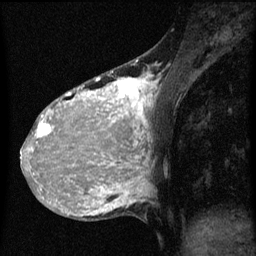
Breast MRI (dynamic contrast-enhanced), one sagittal slice. Slice 20 of 60 in the series (ordered by position). Dynamic contrast-enhanced series, image 2 of 3 at this slice position (ordered by acquisition). 1.5 T. TE 4.2 ms, TR 8 ms. 256 × 256 image matrix, field of view 180 × 180 mm. Patient: female, 36 years.
Outlined on this slice (semi-automatically segmented with operator editing):
- analysis volume of interest (the breast-tissue region the enhancement analysis was run in; not a lesion): bounding box (x1, y1, x2, y2) in pixels: (32, 68, 159, 161)
- tumour enhancement mask (voxels above the 70 % enhancement threshold inside the analysis volume of interest): (32, 72, 157, 161)